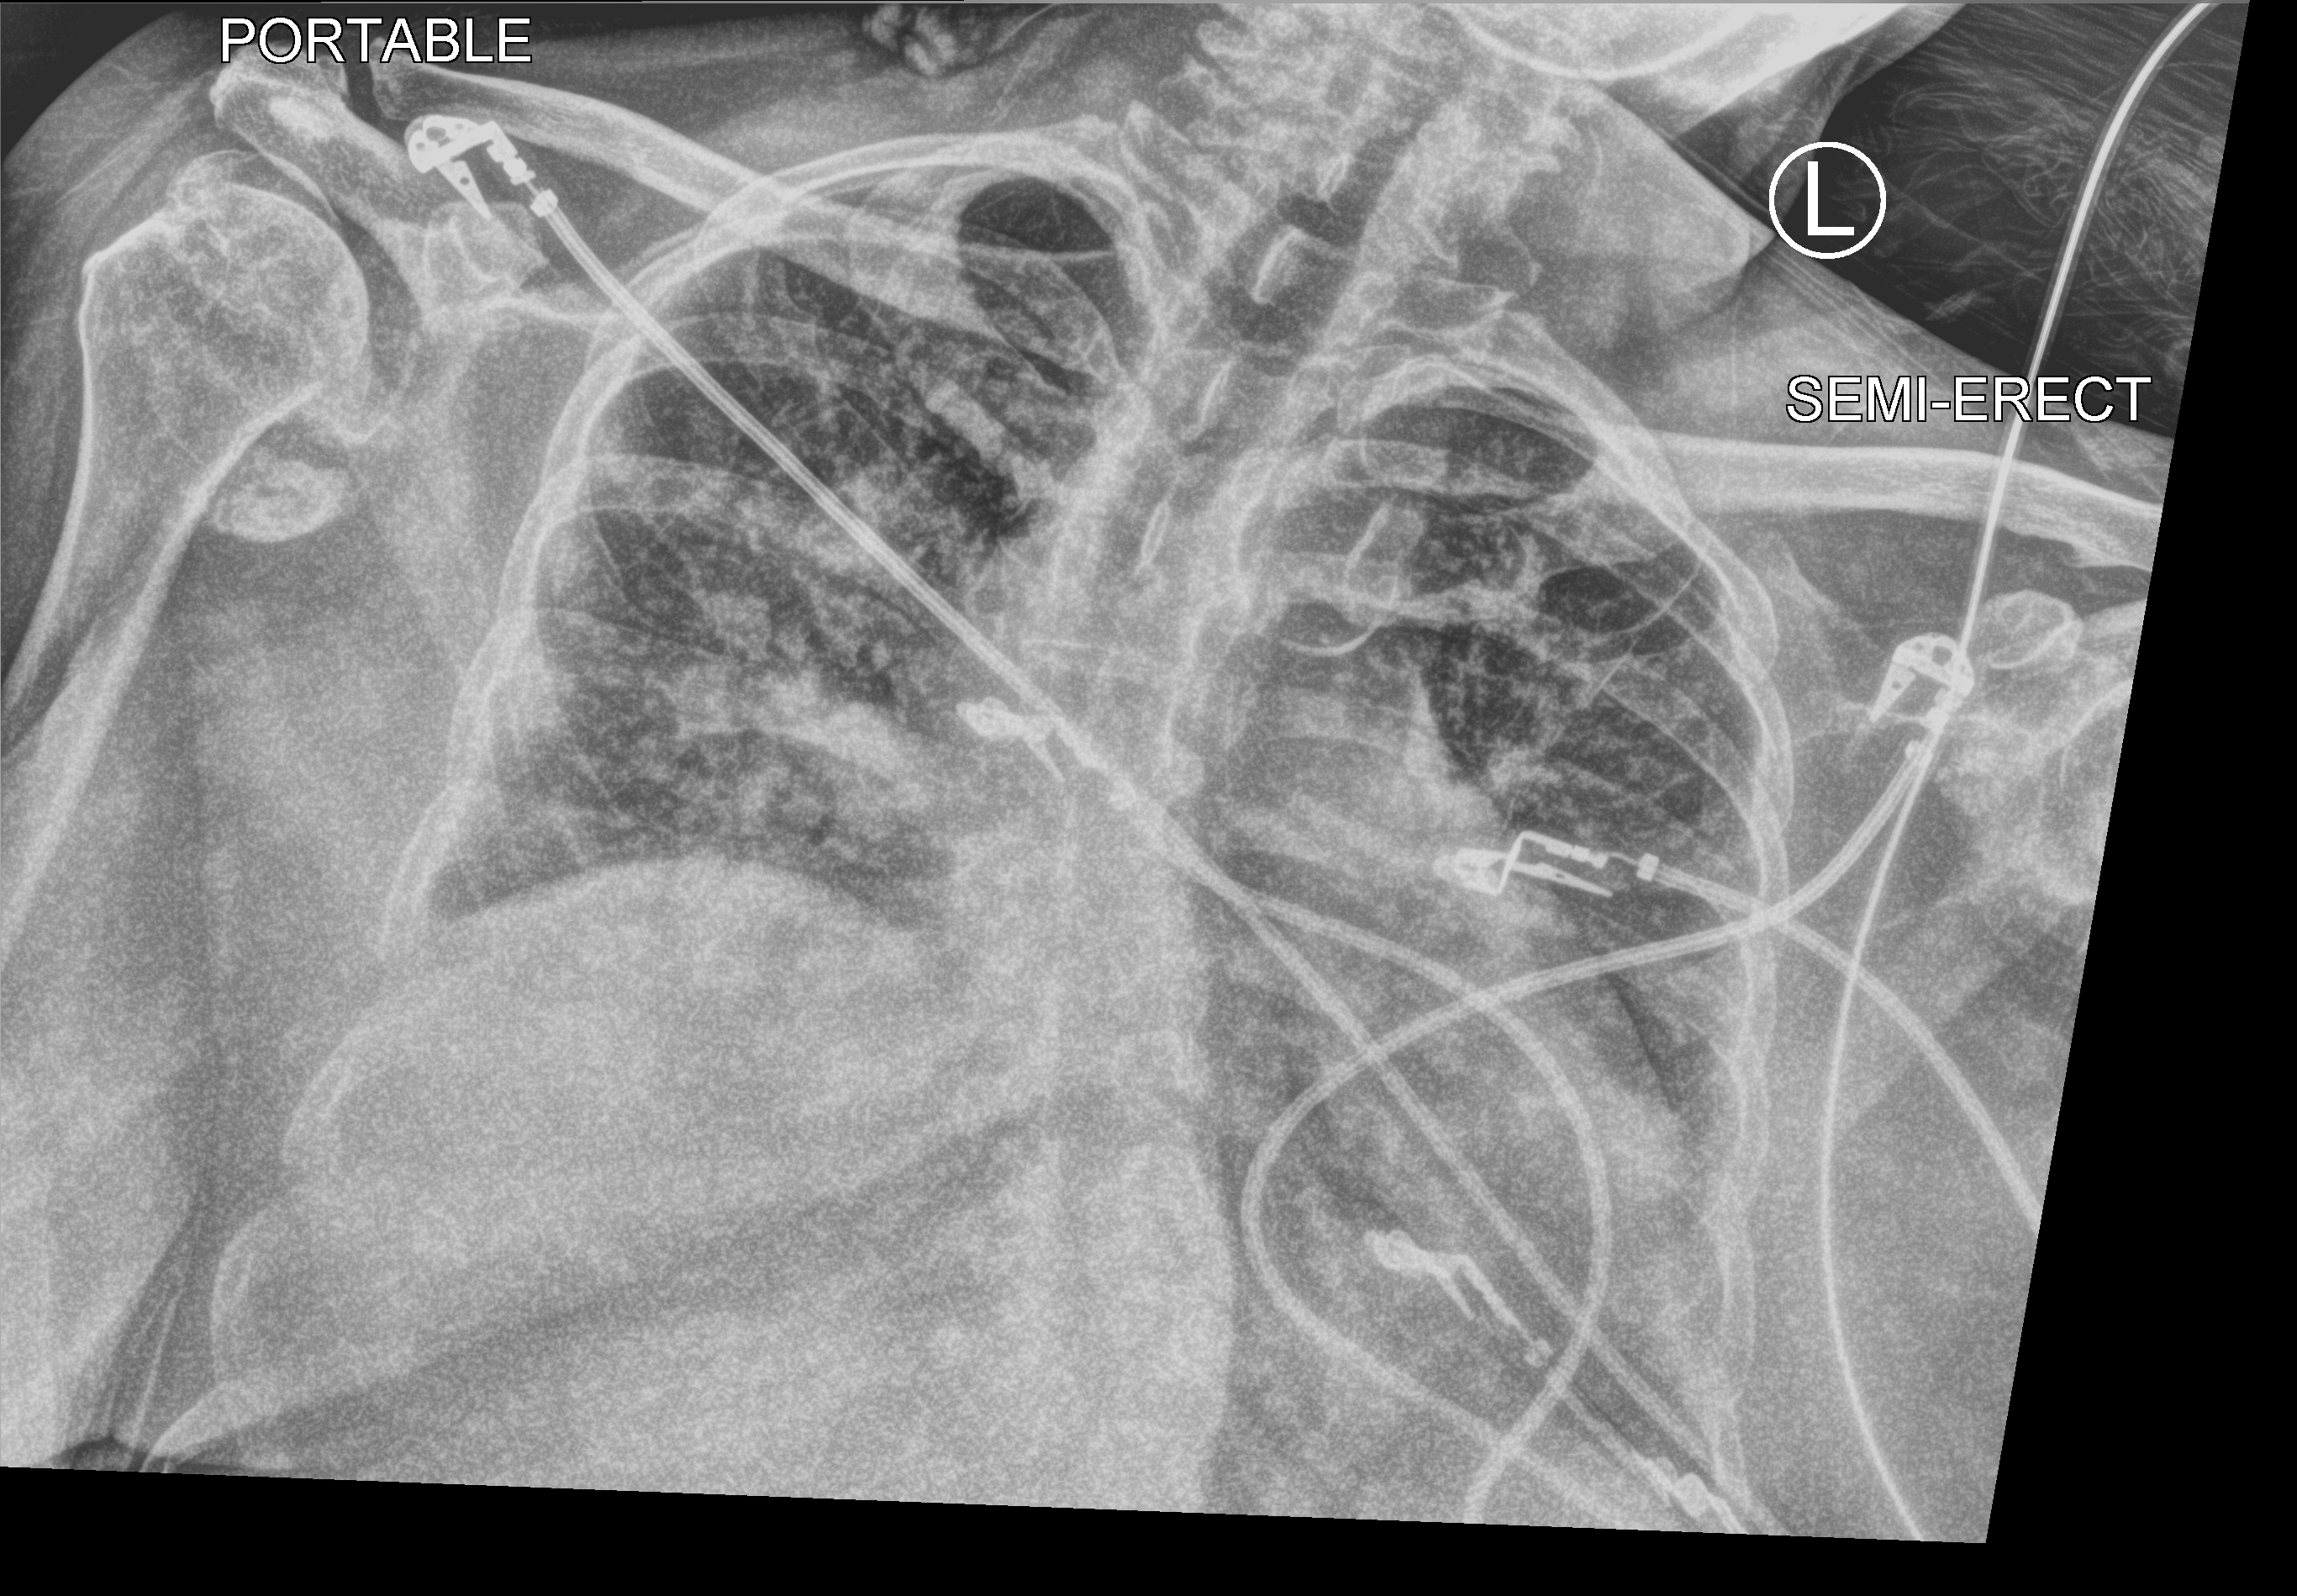
Bedside chest radiograph (computed radiography), anteroposterior (AP) projection. Patient hospitalised with COVID-19; female, aged 60–74 years.
Admission-level facts for this patient (not findings on this image; timing relative to this image not recorded): smoking status (admission record): never.